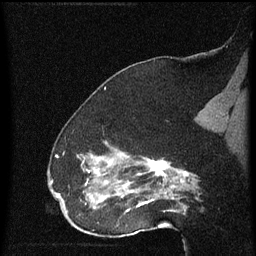
Breast MRI (dynamic contrast-enhanced), one sagittal slice; position 39 of 60 along the scan axis; dynamic contrast-enhanced series, image 2 of 4 at this slice position (ordered by acquisition); 1.5 T; TE 4.2 ms, TR 8 ms; 2 mm slice thickness; 256 × 256 image matrix, field of view 180 × 180 mm. Patient: female, 52 years.
Outlined on this slice (semi-automatically segmented with operator editing):
- analysis volume of interest (the breast-tissue region the enhancement analysis was run in; not a lesion): box from (x=73, y=148) to (x=172, y=219) px
- tumour enhancement mask (voxels above the 70 % enhancement threshold inside the analysis volume of interest): (x=85, y=158)–(x=172, y=211)